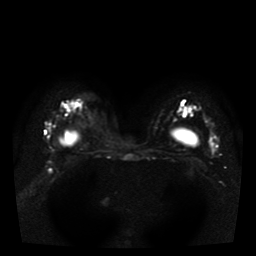
Breast MRI, one axial slice; position 28 of 41 along the scan axis; diffusion-weighted series; image 2 of 3 stored at this slice position (different b-values; order by instance number); 1.5 T; 5 mm slice thickness; 256 × 256 image matrix, field of view 330 × 330 mm. Female patient.
Structures marked on this image (outlined manually by an expert reader):
- tumour on diffusion-weighted imaging: box from (x=209, y=137) to (x=215, y=152) px